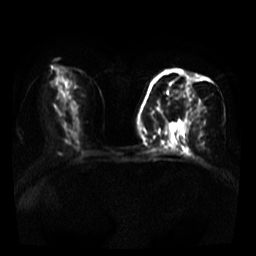
Breast MRI, one axial slice. Slice 16 of 39 in the series (ordered by position). Diffusion-weighted series; image 2 of 4 stored at this slice position (different b-values; order by instance number). 3 T. 256 × 256 image matrix, field of view 320 × 320 mm. Female patient.
Annotated regions visible in this slice (outlined manually by an expert reader):
- tumour on diffusion-weighted imaging: bounding box [x1, y1, x2, y2] px = [182, 74, 204, 110]